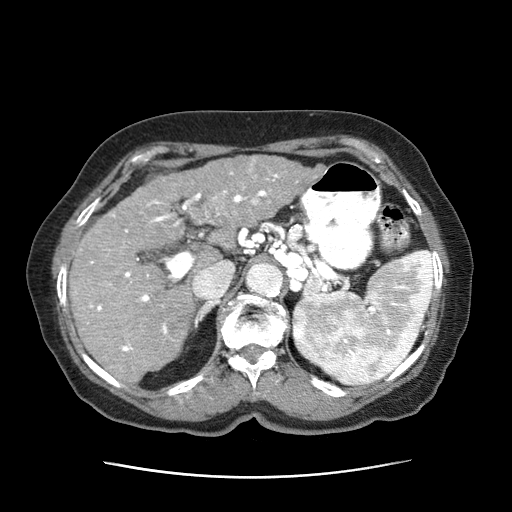
Contrast-enhanced abdominal CT (liver protocol), one axial slice; reconstruction kernel STANDARD; 120 kVp; intravenous contrast given; soft-tissue window (W 400 / L 40 HU); 2.5 mm slice thickness; 512 × 512 image matrix, field of view 360 × 360 mm. Female patient, age 79 years. From the clinical record (not read from this slice): diagnosis: hepatocellular carcinoma (patient treated with transarterial chemoembolisation; whether this scan precedes or follows treatment is not stated here); TNM stage (as recorded): Stage-II; Child-Pugh class: B; tumour differentiation: well differentiated; tumour size: 5 cm.
Annotated regions visible in this slice (semi-automatically segmented with operator editing):
- abdominal aorta: bounding box [x1, y1, x2, y2] px = [246, 263, 283, 297]
- liver parenchyma outside the tumour (the mass and vessels are separate outlines, so this box may not span the whole liver): [70, 177, 239, 383]
- mass: [155, 154, 322, 229]
- liver vessels: [87, 172, 285, 352]